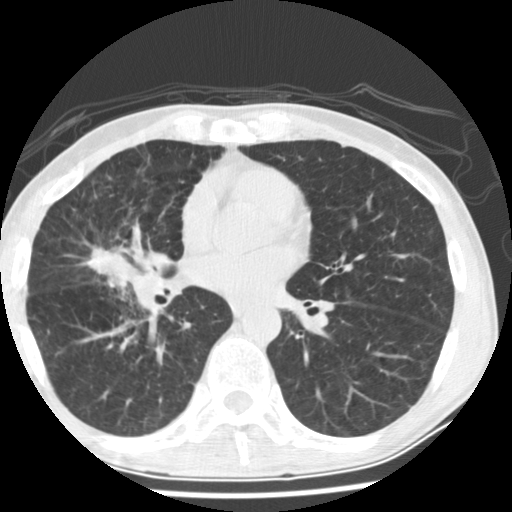
Low-dose screening chest CT, one axial slice; position 79 of 162 along the scan axis; 120 kVp; lung window (W 1500 / L -600 HU); 512 × 512 image matrix, field of view 310 × 310 mm.
Structures marked on this image (manually delineated by an expert):
- lesion 1 (tumor, middle lobe of right lung): box from (x=72, y=247) to (x=124, y=281) px